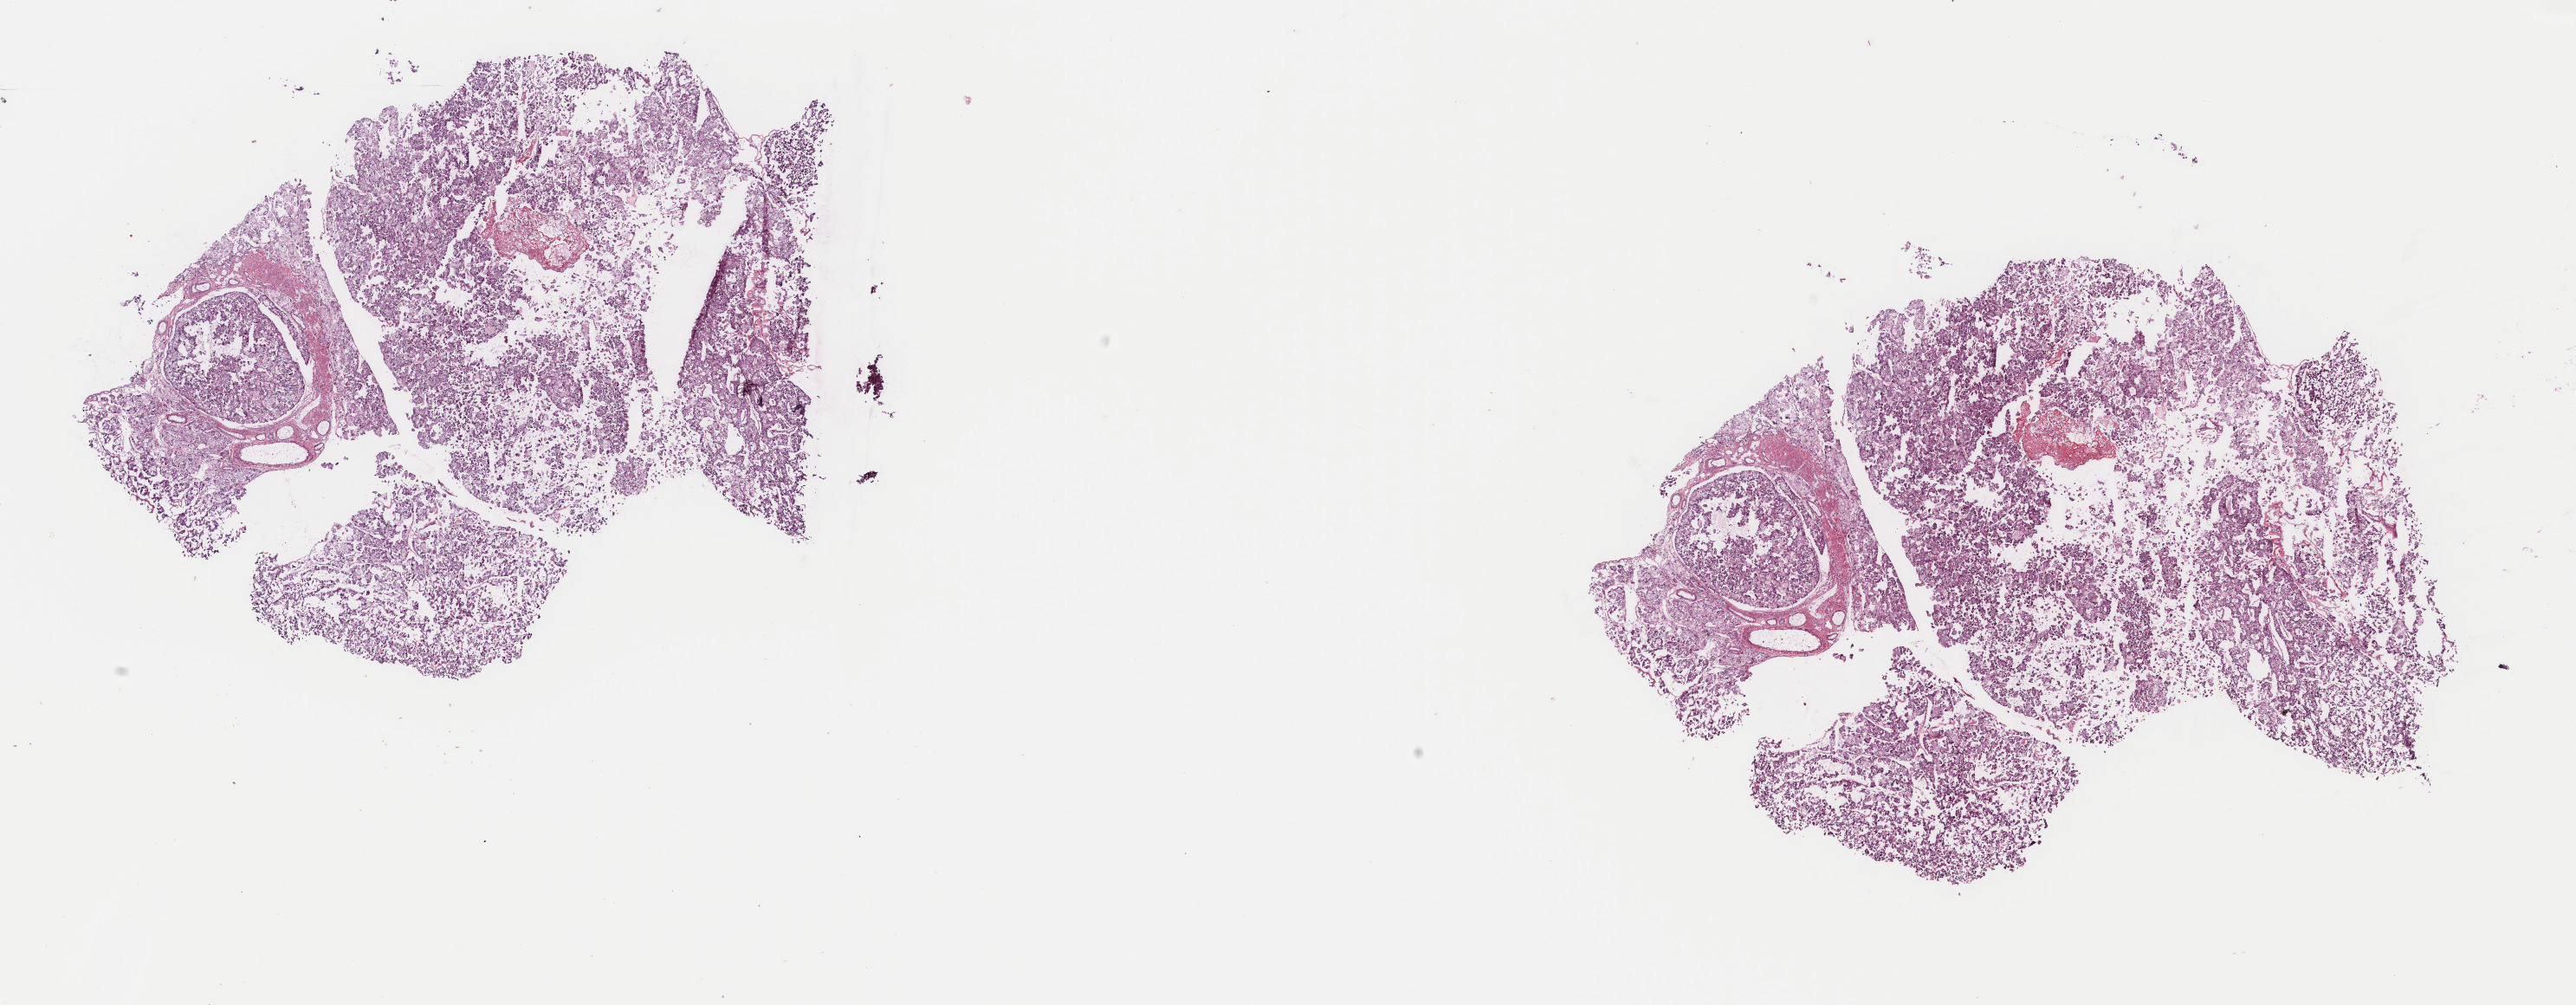
H&E whole-slide image — shown as a low-resolution overview of the whole scanned area (about 23.6 x 9.2 mm); frozen section; sample: primary tumour, kidney. Male, age 57 years at initial diagnosis.
Pathologic diagnosis: Renal cell carcinoma, chromophobe type.